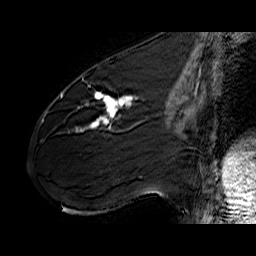
Breast MRI (dynamic contrast-enhanced), one sagittal slice; dynamic contrast-enhanced series, time point 2 of 6 at this slice position (early post-contrast); 1.5 T; TE 6.4 ms, TR 32.9 ms; 256 × 256 image matrix. Female patient. From the clinical record (not read from this slice): setting: breast cancer imaged before/during neoadjuvant chemotherapy; receptor status: HER2-positive.
Structures marked on this image (semi-automatic segmentation, software-assisted and operator-edited):
- analysis volume of interest (the breast-tissue region the enhancement analysis was run in; not a lesion): bounding box (x1, y1, x2, y2) in pixels: (61, 77, 141, 142)
- tumour enhancement mask (voxels above the 100 % enhancement threshold inside the analysis volume of interest): (61, 92, 137, 132)